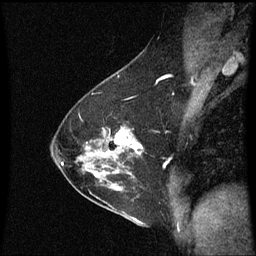
Breast MRI (dynamic contrast-enhanced), one sagittal slice. Position 39 of 60 along the scan axis. Dynamic contrast-enhanced series, image 2 of 3 at this slice position (ordered by acquisition). 1.5 T. TE 4.2 ms, TR 8.9 ms. 2 mm slice thickness. 256 × 256 image matrix, field of view 200 × 200 mm. Female patient, age 54 years. From the clinical record (not read from this slice): setting: breast cancer imaged before/during neoadjuvant chemotherapy; receptor status: HER2-positive.
Structures marked on this image (semi-automatically segmented with operator editing):
- analysis volume of interest (the breast-tissue region the enhancement analysis was run in; not a lesion): box from (x=102, y=124) to (x=144, y=169) px
- tumour enhancement mask (voxels above the 70 % enhancement threshold inside the analysis volume of interest): (x=114, y=130)–(x=142, y=155)